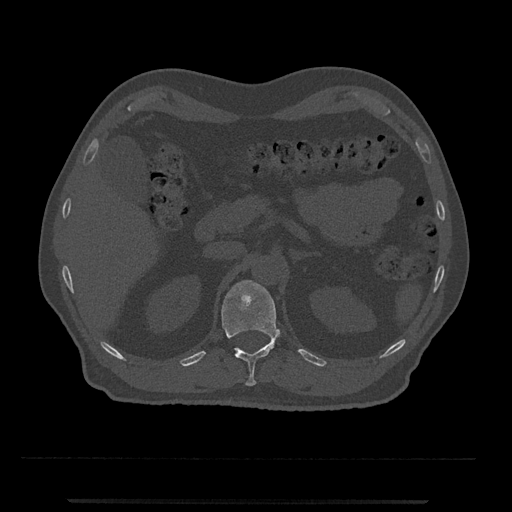
CT including the spine, one axial slice; reconstruction kernel Br40s/3; 120 kVp; bone window (W 1800 / L 400 HU); 0.5 mm slice thickness; 512 × 512 image matrix. Patient: male, 63 years. Case-level facts recorded for this patient, not image findings: primary cancer: prostate.
Outlined on this slice (semi-automatic segmentation, software-assisted and operator-edited):
- T12 vertebra: bounding box (x1, y1, x2, y2) in pixels: (221, 280, 281, 386)